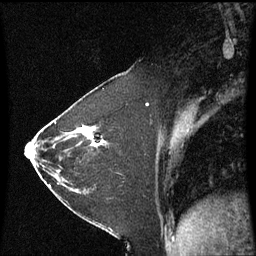
Breast MRI (dynamic contrast-enhanced), one sagittal slice. Slice 33 of 60 in the series (ordered by position). Dynamic contrast-enhanced series, image 2 of 3 at this slice position (ordered by acquisition). 1.5 T. TE 4.2 ms, TR 8.9 ms. 256 × 256 image matrix, field of view 200 × 200 mm. Patient: female, 37 years. From the clinical record (not read from this slice): setting: breast cancer imaged before/during neoadjuvant chemotherapy; receptor status: HR-positive, HER2-negative.
Structures marked on this image (semi-automatically segmented with operator editing):
- analysis volume of interest (the breast-tissue region the enhancement analysis was run in; not a lesion): box from (x=60, y=102) to (x=122, y=181) px
- tumour enhancement mask (voxels above the 70 % enhancement threshold inside the analysis volume of interest): (x=96, y=130)–(x=110, y=145)